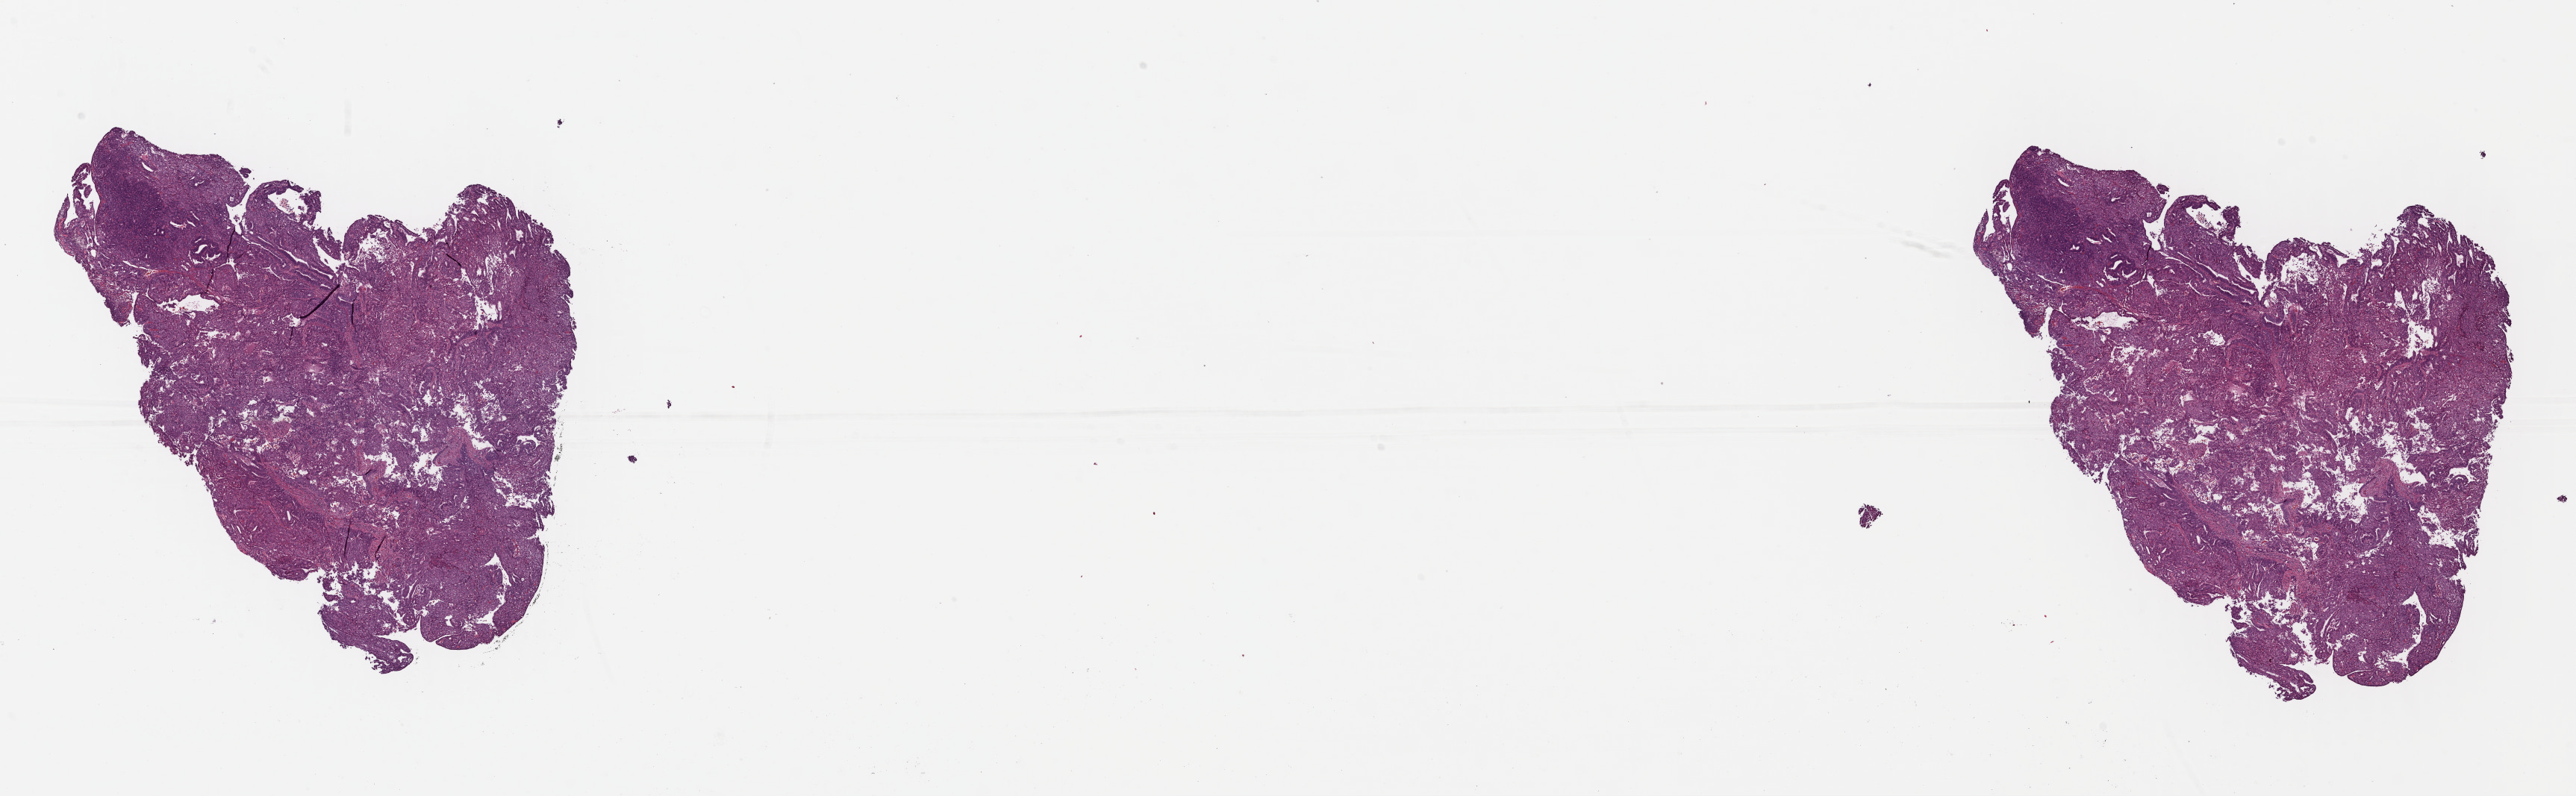
Whole-slide histology image, H&E-stained — shown as a low-resolution overview of the whole scanned area (about 27.1 x 8.4 mm). FFPE section. Primary tumour sample from the uterus. Female patient; age at initial diagnosis 47 years. Histologic grade: G2 (moderately differentiated).
* FIGO stage: IB
* histologic diagnosis: Endometrioid adenocarcinoma, NOS (endometrium)